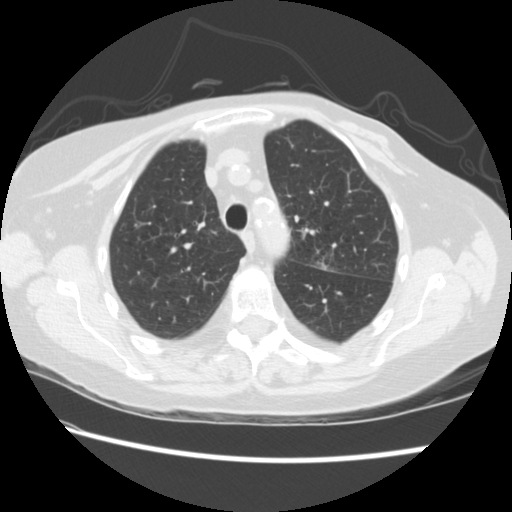
Chest CT (low-dose screening protocol), one axial image; baseline annual screen; lung window (W 1500 / L -600 HU); 2.5 mm slice thickness; standard (soft-tissue) reconstruction kernel (STANDARD); slice 62 of 224 in the series; 512 × 512 image matrix. Female participant, aged 74 years at enrolment. Former smoker at enrolment.
• Lesion marked by an expert reader, bounding box (x1, y1, x2, y2) in pixels: (296, 233, 347, 279).
• The screening reader recorded 2 non-calcified nodules or masses ≥4 mm on this exam (left upper lobe, right lower lobe); which of them this box marks is not recorded.
• Later outcome: lung cancer diagnosed 309 days after this screen — non-small cell carcinoma, left upper lobe, stage IV (AJCC 6th edition).